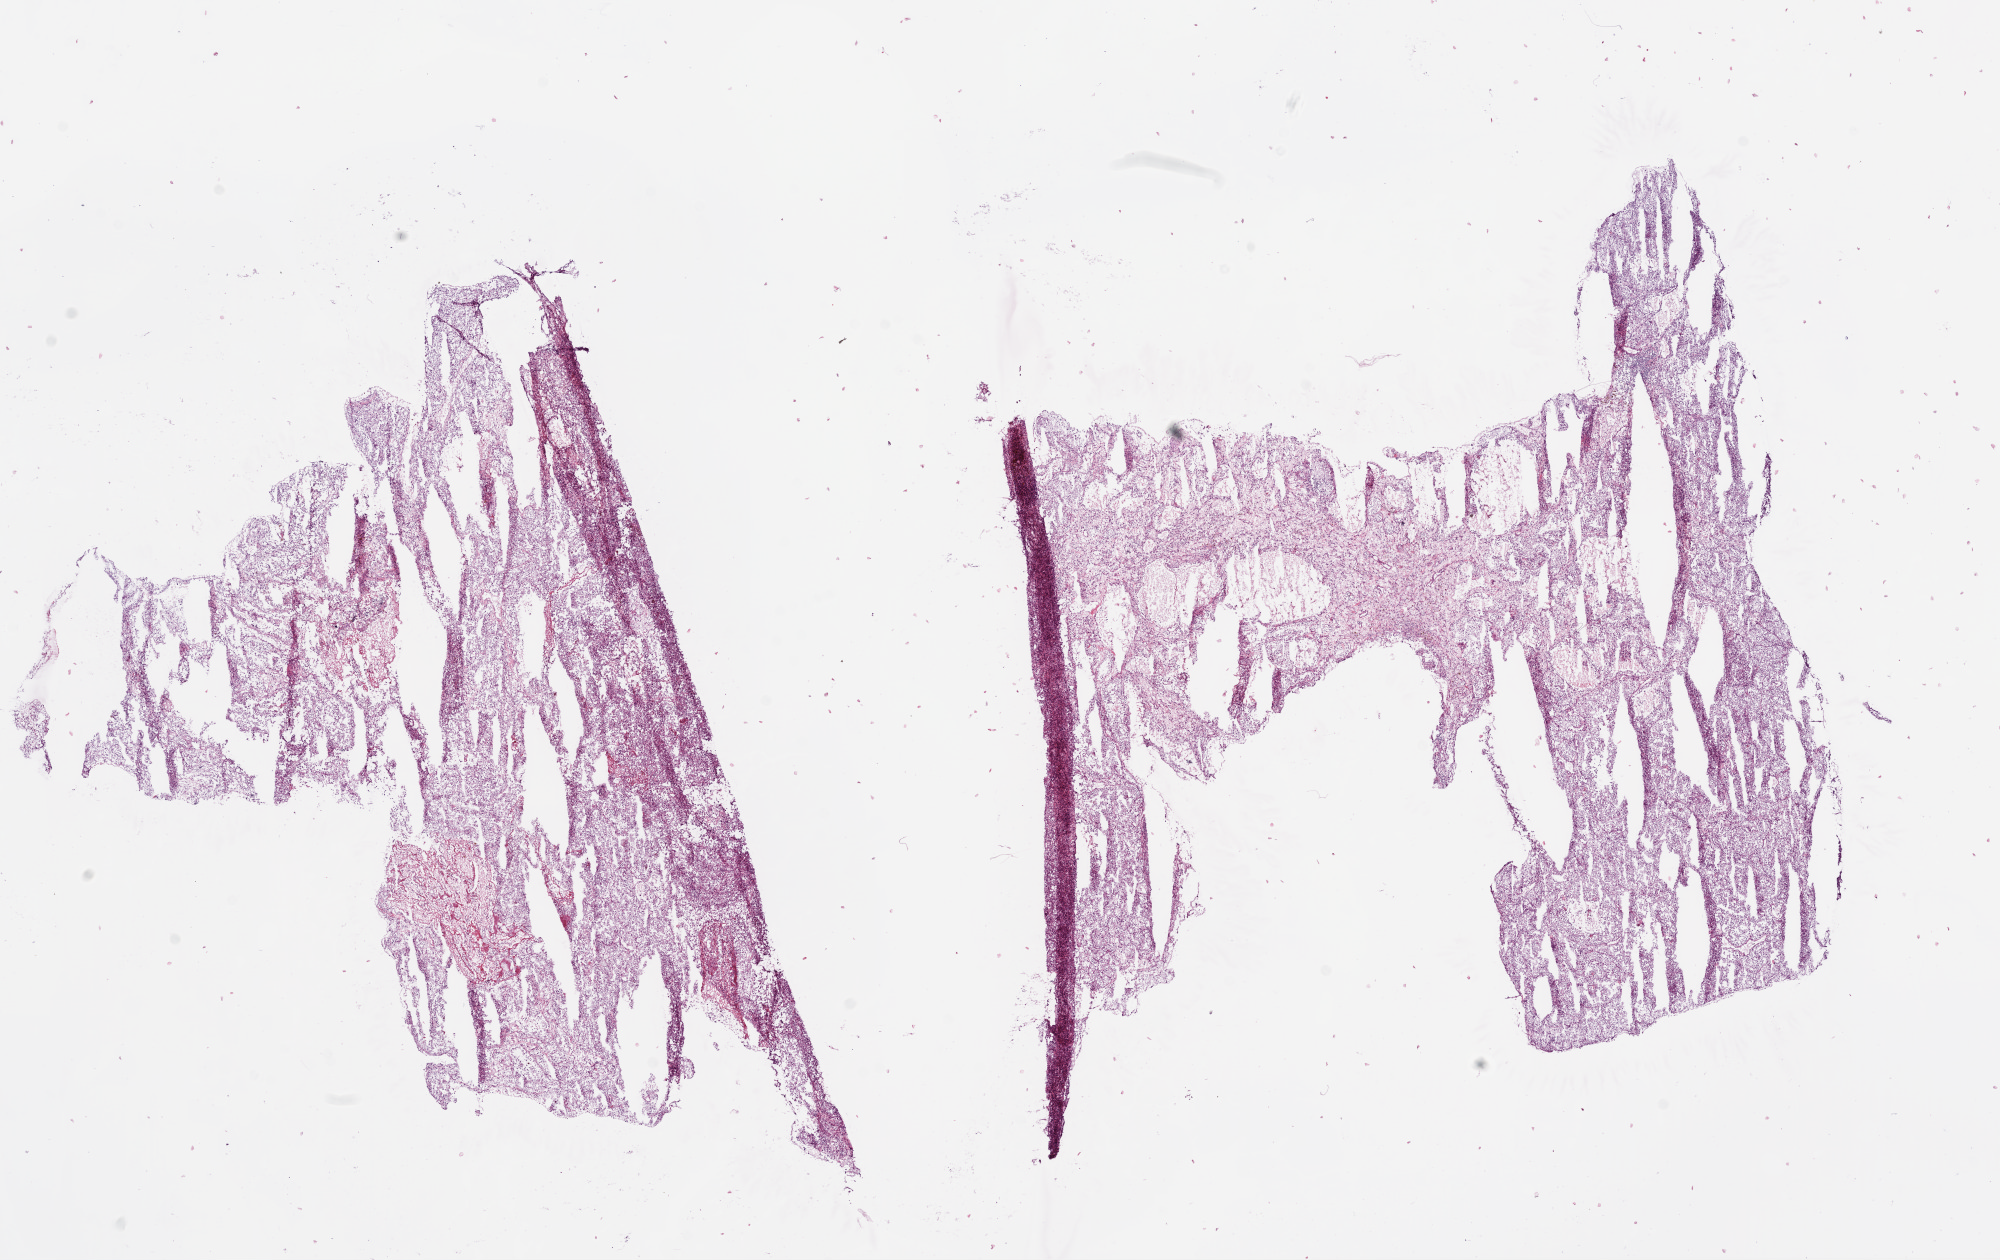
Digitized H&E-stained tissue section (whole slide), low-resolution overview of the scanned area, about 16.0 x 10.1 mm (from a 20x scan), frozen section, primary tumour sample from the kidney. Patient: male, age at initial diagnosis 53 years. Histologic grade: G3 (poorly differentiated). Pathologist review of this section (percent, as recorded): tumour cells 90%, tumour nuclei 80%, normal cells 0%, stromal cells 10%, necrosis 0%.
AJCC pathologic stage: I. Pathologic diagnosis: Clear cell adenocarcinoma, NOS.